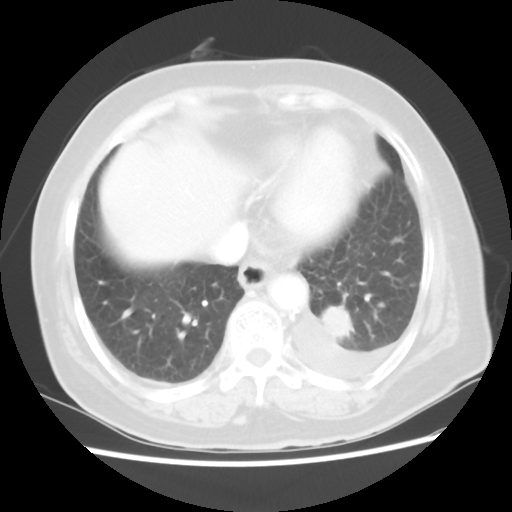
Chest CT, one axial slice; reconstruction kernel STANDARD; 100 kVp; lung window (W 1500 / L -600 HU); 512 × 512 image matrix, field of view 343 × 343 mm. Patient: female, 68 years. From the clinical record (not read from this slice): clinical TNM (as recorded): T1c N0 M1.
Outlined on this slice (rectangle marked by the reading radiologist):
- lung tumour (recorded histology: adenocarcinoma): bounding box (x1, y1, x2, y2) in pixels: (320, 303, 359, 341)